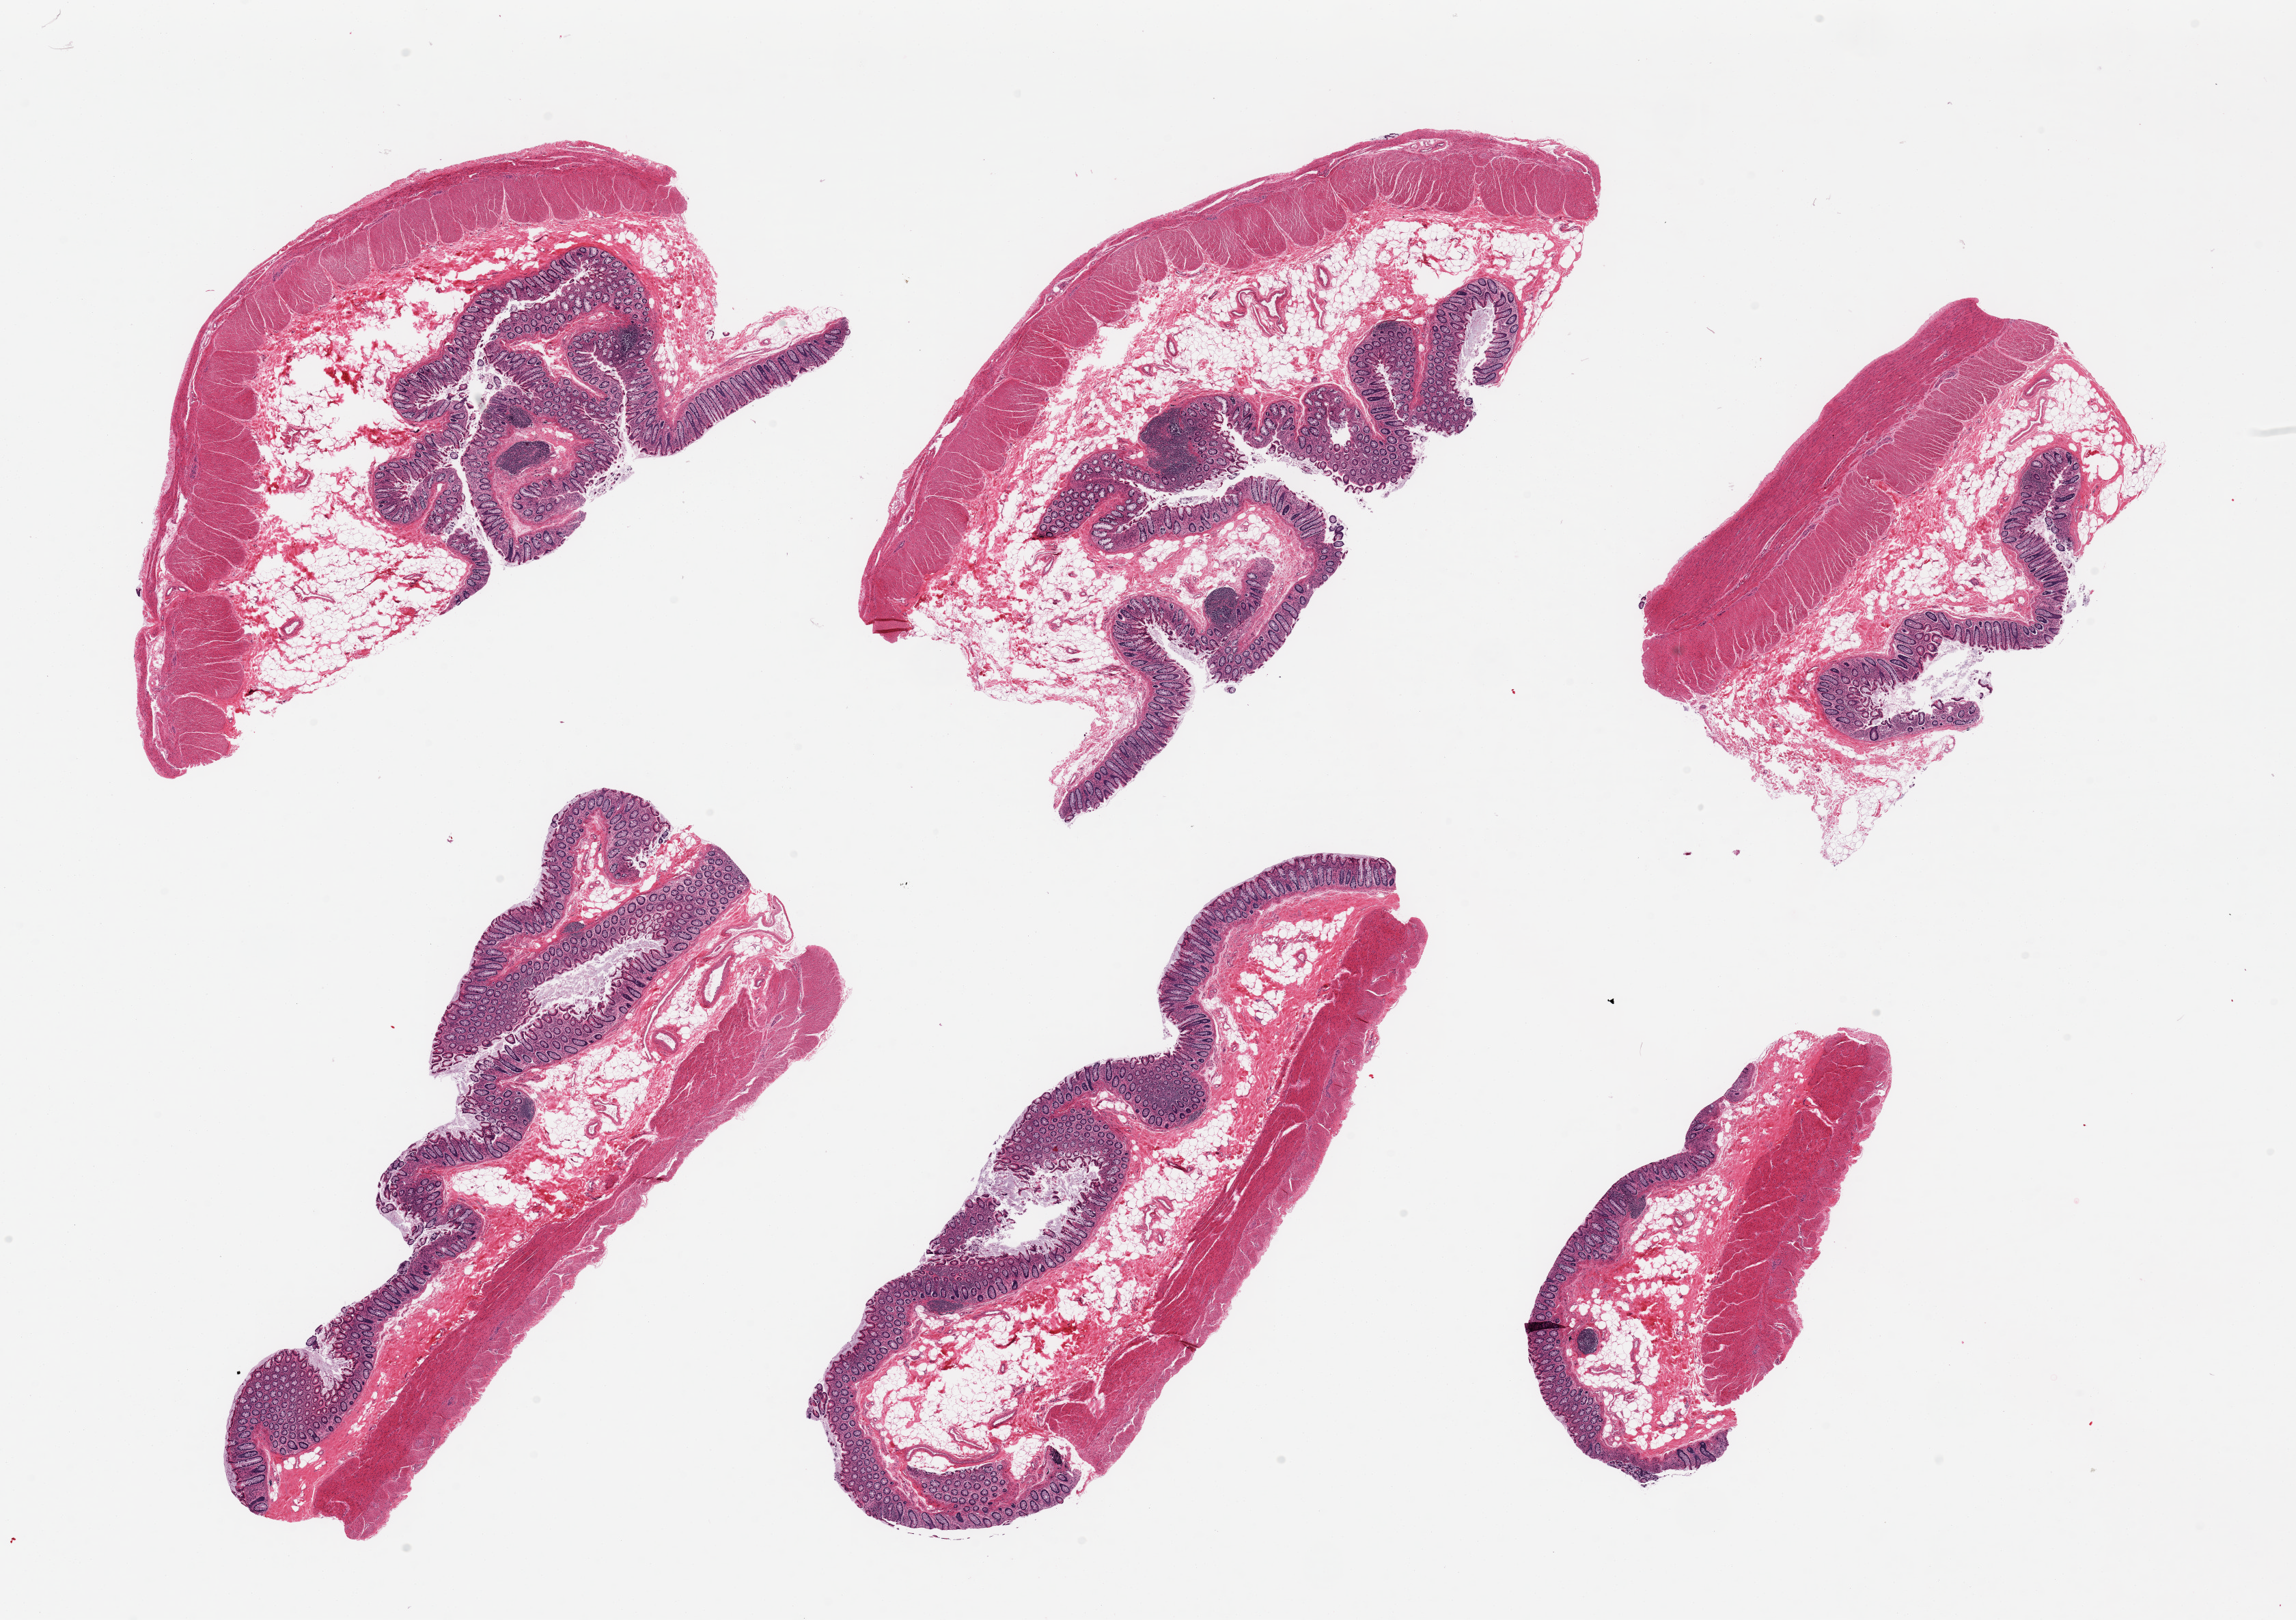
Digitized hematoxylin and eosin (H&E)-stained section, low-resolution overview of the scanned area, about 26.6 x 18.8 mm (acquisition: 20x scan), PAXgene-fixed paraffin-embedded (PFPE) section, sampled site (target tissue): transverse colon, tissue donor sample. Donor: male.
Reviewer comment on this tissue sample: 6 pieces, target mucosa up to ~0.4mm, 15-20% thickness.